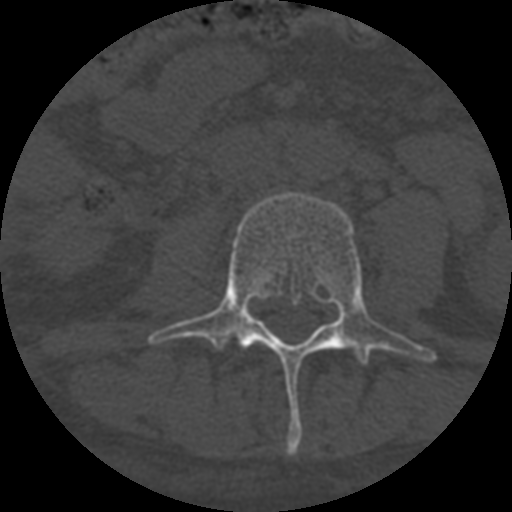
CT including the spine, one axial slice; reconstruction kernel STANDARD; 120 kVp; one of 3 acquisitions stored at this slice position; bone window (W 1800 / L 400 HU); 1.25 mm slice thickness; 512 × 512 image matrix, field of view 160 × 160 mm. Patient age 55 years. From the clinical record (not read from this slice): primary cancer: colon.
Outlined on this slice (semi-automatically segmented with operator editing):
- L3 vertebra: bounding box (x1, y1, x2, y2) in pixels: (148, 192, 437, 454)